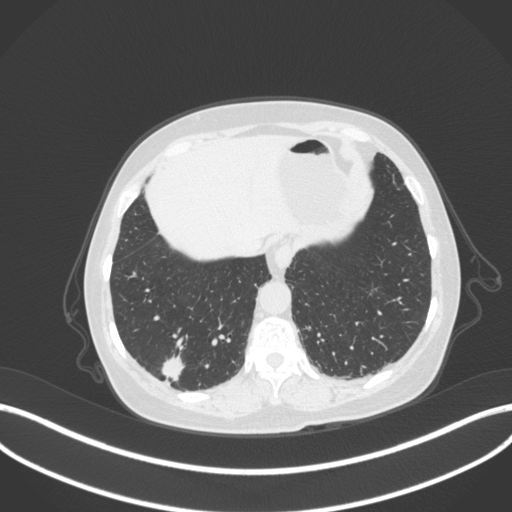
Chest CT, one axial slice. Slice 59 of 340 in the series (ordered by position). Reconstruction kernel B31f. 120 kVp. Lung window (W 1500 / L -600 HU). 1 mm slice thickness. 512 × 512 image matrix, field of view 400 × 400 mm. Female patient, age 69 years. Case-level facts recorded for this patient, not image findings: clinical TNM (as recorded): T1b N0 M0; histopathological grade: G2-3.
Outlined on this slice (bounding box drawn by a radiologist):
- lung tumour (recorded histology: adenocarcinoma): box from (x=154, y=351) to (x=187, y=385) px